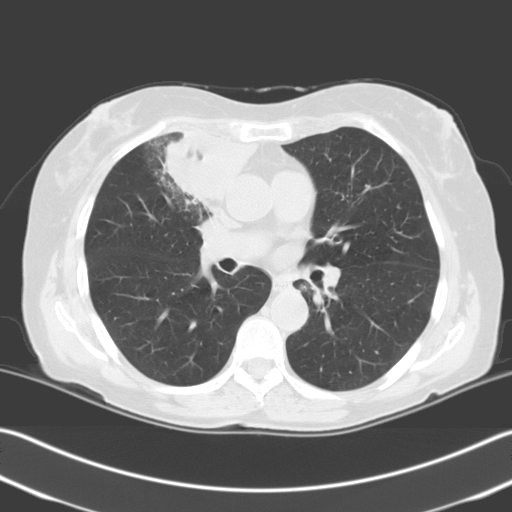
Low-dose screening chest CT, one axial slice; slice 122 of 204 in the series (ordered by position); 140 kVp; lung window (W 1500 / L -600 HU); 3.2 mm slice thickness; 512 × 512 image matrix.
Outlined on this slice (manually delineated by an expert):
- lesion 1 (tumor, upper lobe of right lung): bounding box <163,131,257,208> (left, top, right, bottom; pixels)